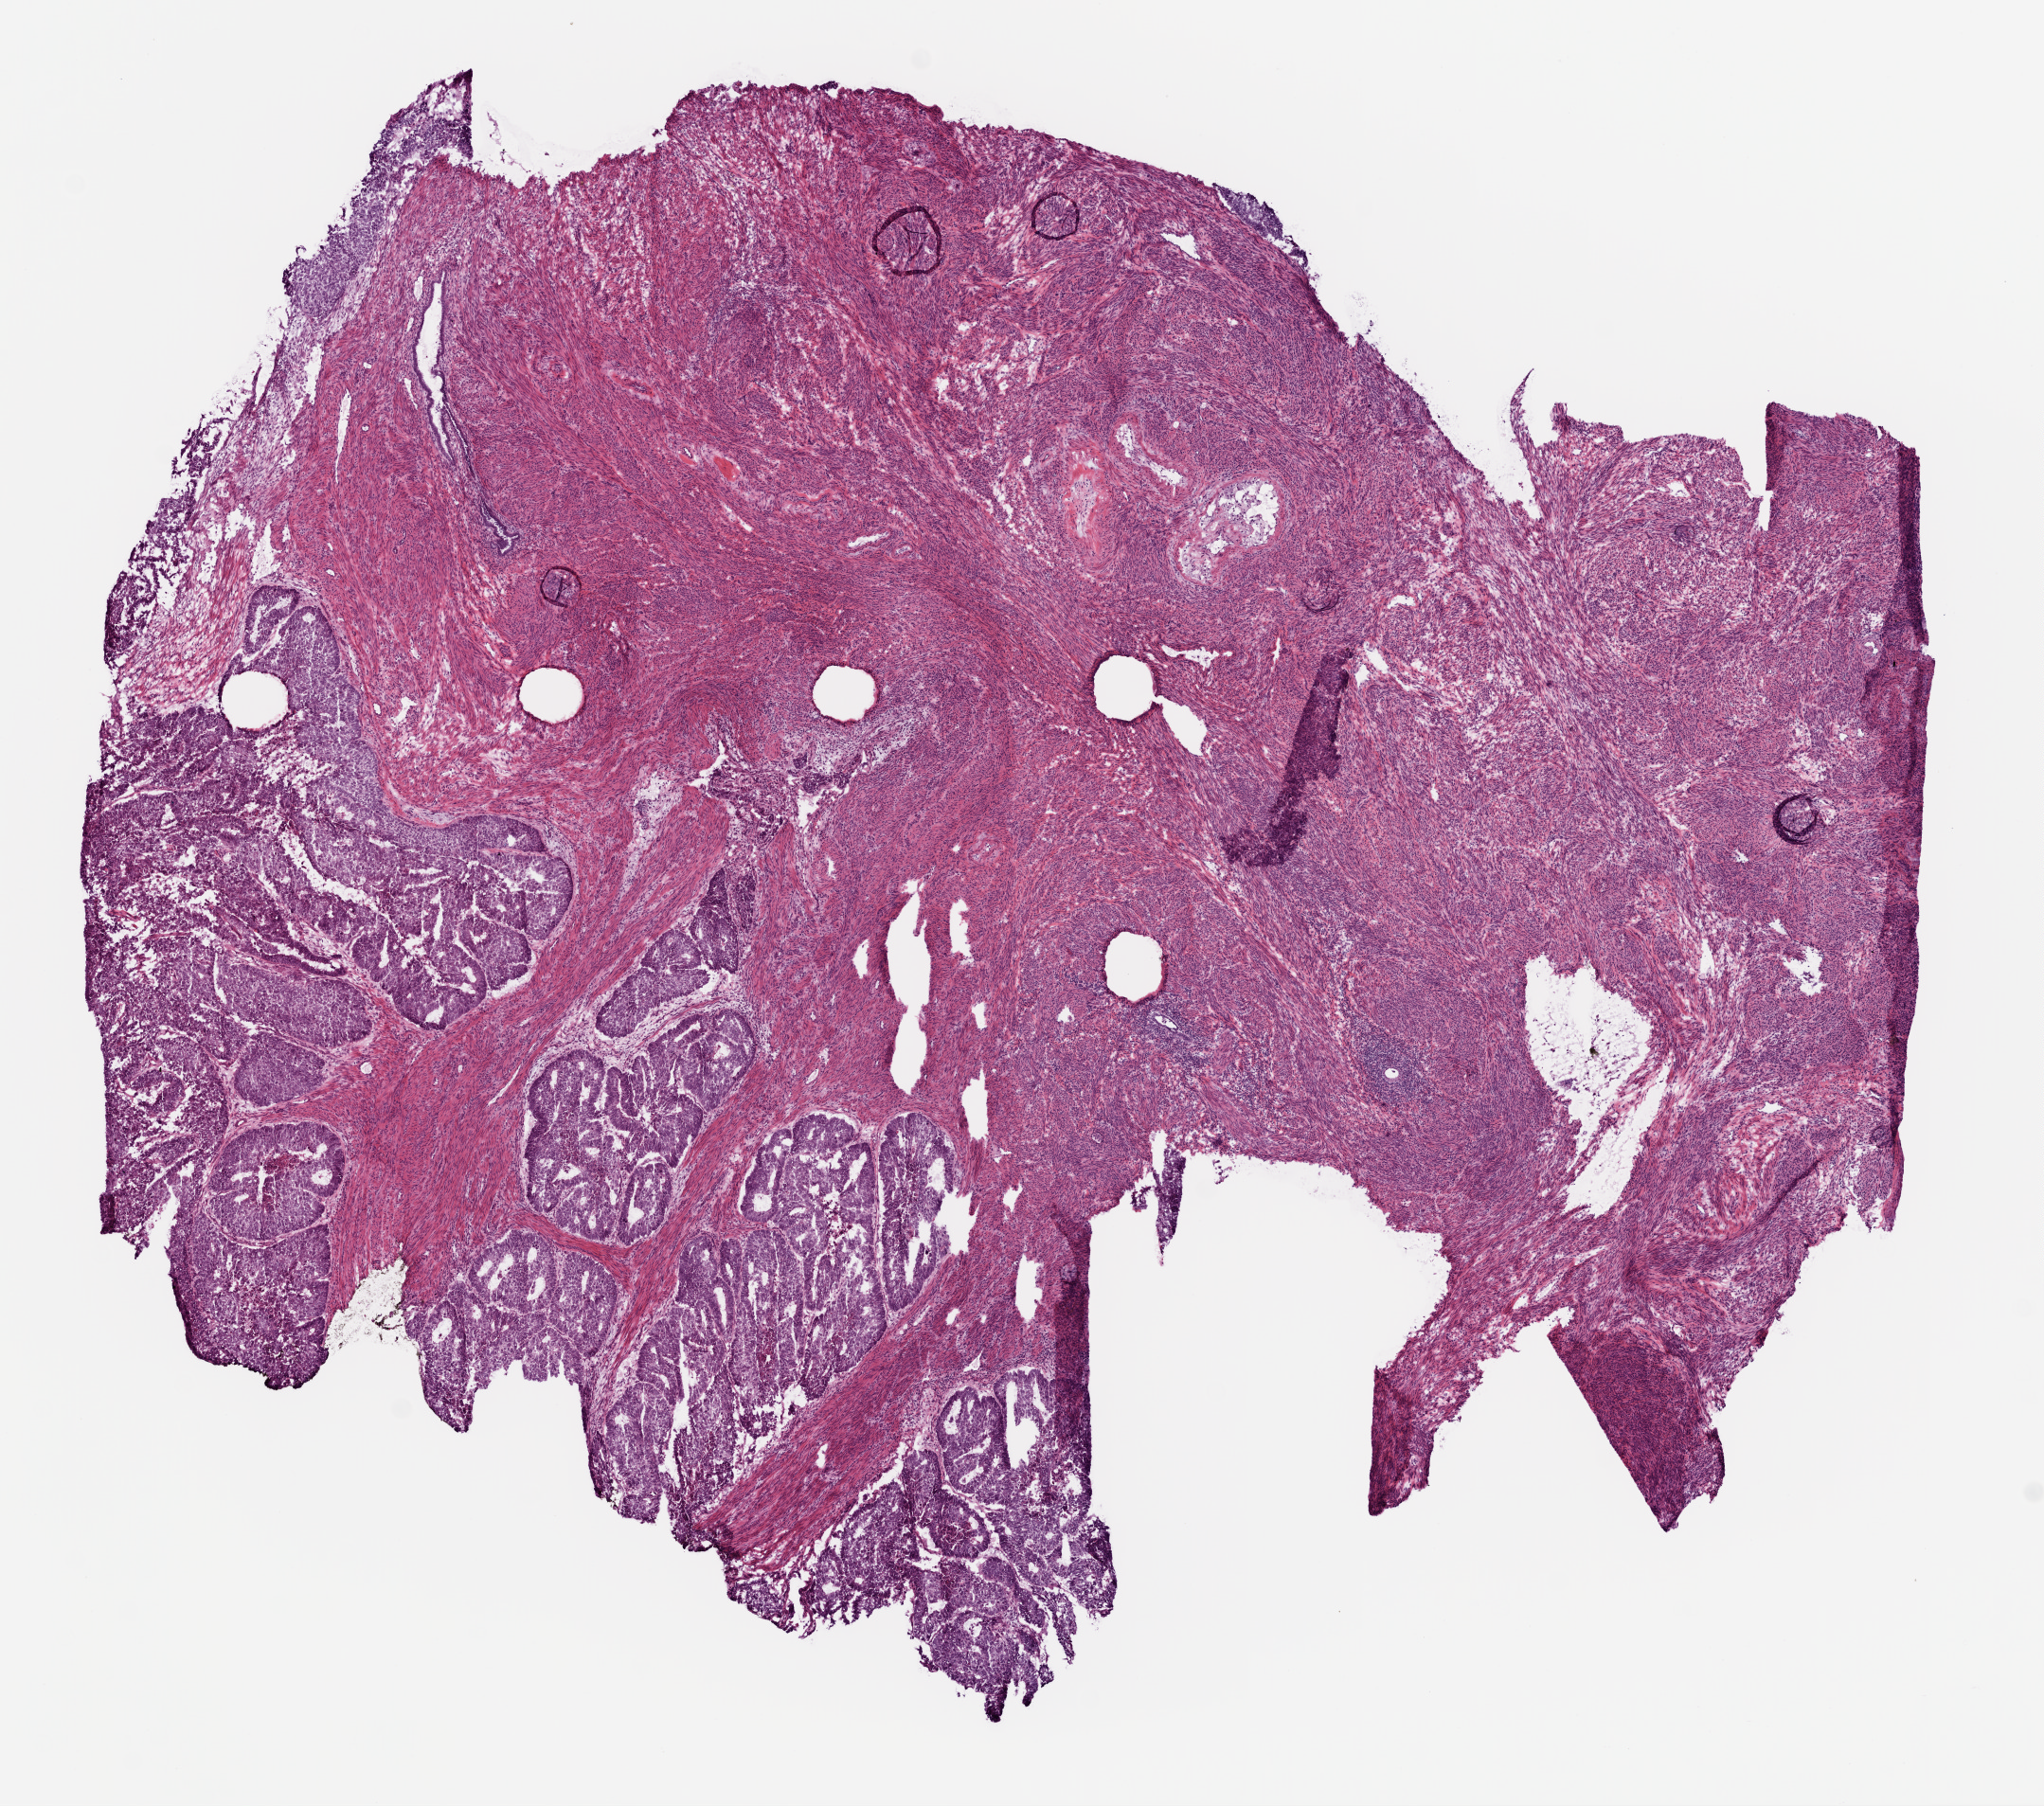
Whole-slide histology image, H&E-stained — whole scanned area (about 8.7 x 7.7 mm, acquisition: 20x scan) shown as a low-resolution overview; frozen section from the top of the tissue portion; primary tumour sample from the uterus. Female patient; age at initial diagnosis 69 years. Histologic grade: G3 (poorly differentiated). Composition of this section per pathologist review: tumour cells 75%, tumour nuclei 80%, normal cells 0%, stromal cells 5%, necrosis 20%. Infiltration values recorded for this section: lymphocyte infiltration 0%, monocyte infiltration 0%, neutrophil infiltration 0%.
Diagnosis: Endometrioid adenocarcinoma, NOS. FIGO stage: IB. Lymph nodes positive (case pathology): 0 of 8 examined.